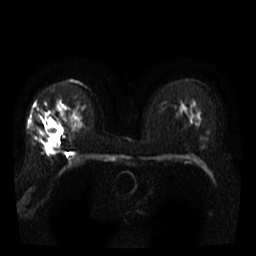
Breast MRI, one axial slice. Diffusion-weighted series; image 2 of 4 stored at this slice position (different b-values; order by instance number). 3 T. 256 × 256 image matrix, field of view 300 × 300 mm. Female patient.
Outlined on this slice (manually delineated by an expert):
- tumour on diffusion-weighted imaging: bounding box (x1, y1, x2, y2) in pixels: (45, 116, 64, 139)